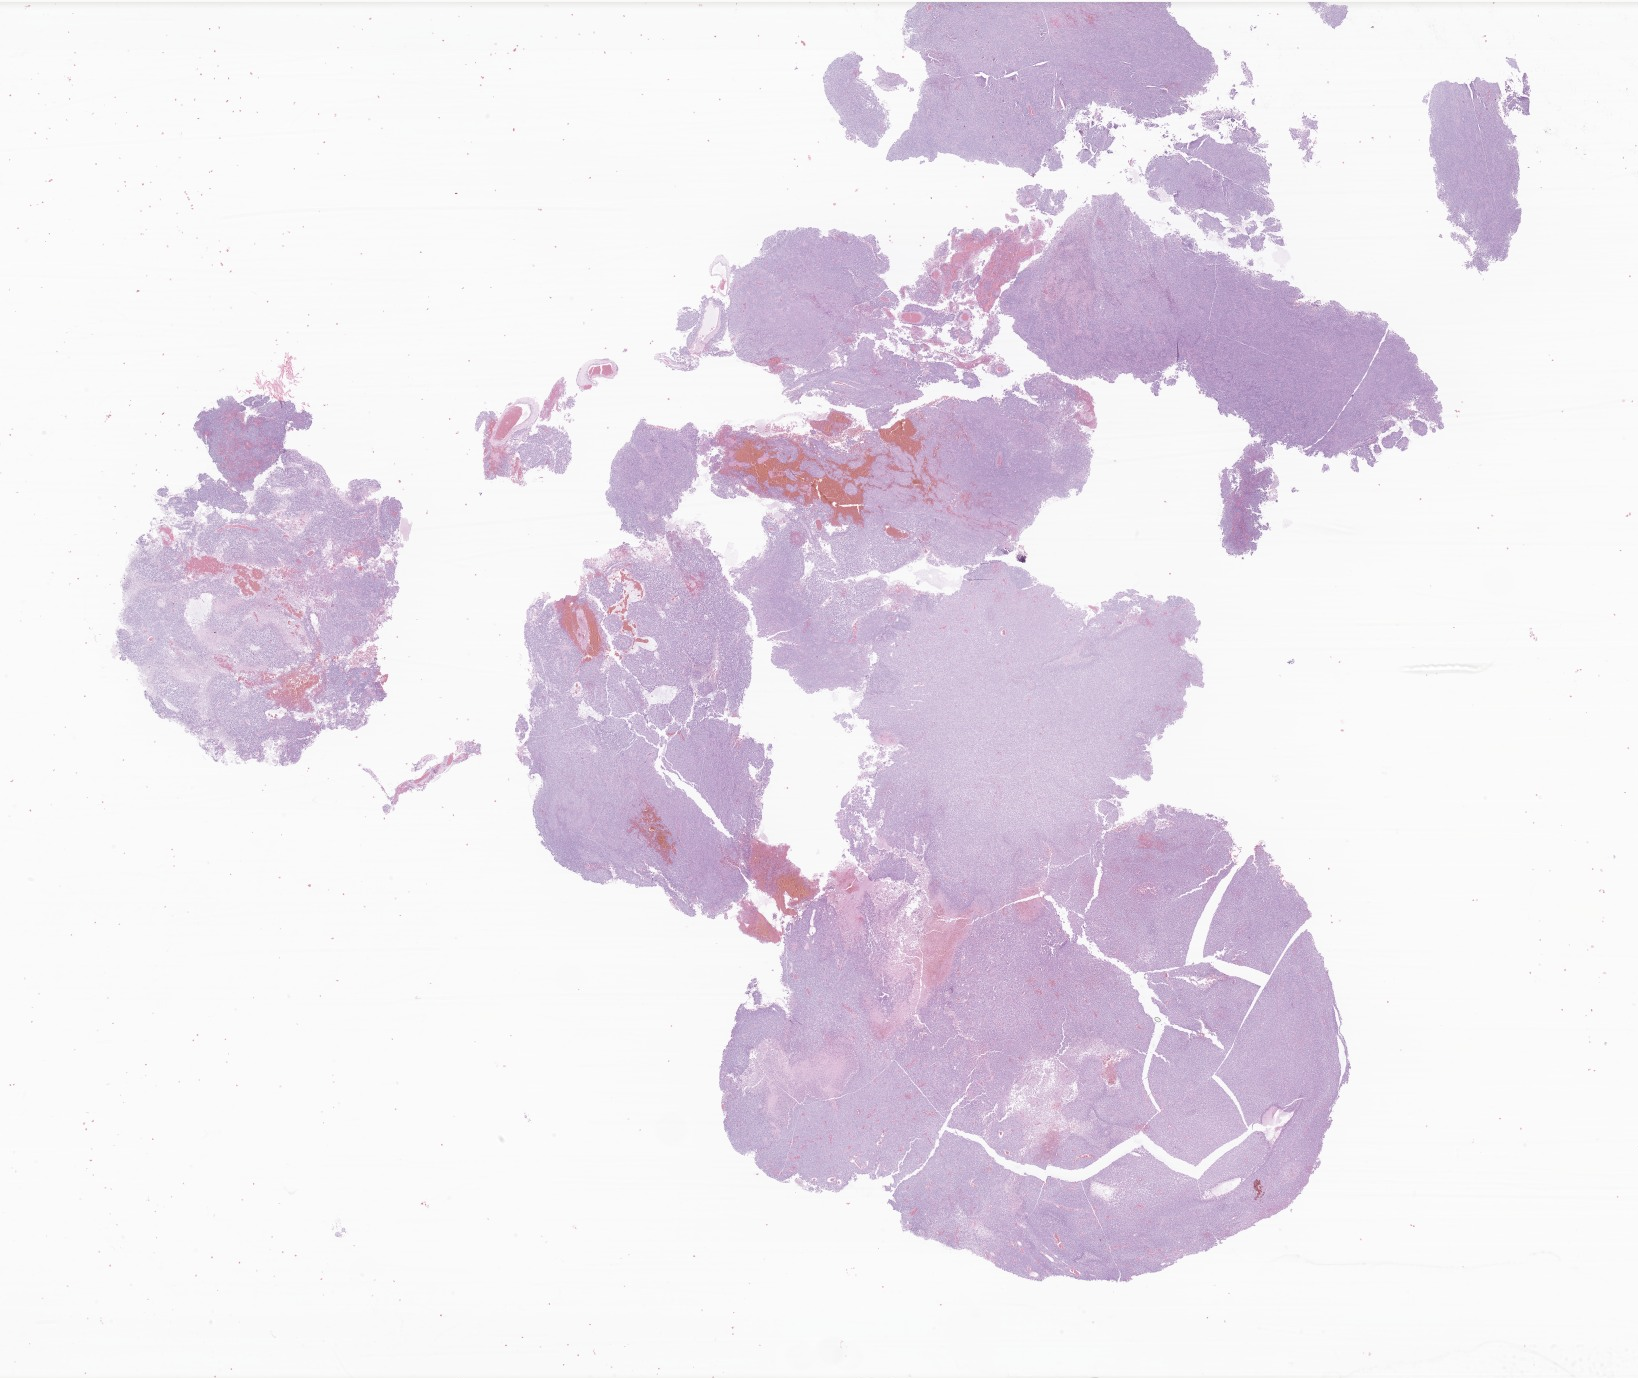
Digitized haematoxylin and eosin-stained section of tumor tissue from the frontal lobe — whole scanned area (about 27.6 x 23.2 mm) shown as a low-resolution overview, formalin-fixed paraffin-embedded section. Patient female; age 780 days (about 2.1 years).
Diagnosis (ICD-O-3 morphology term): Glioma, malignant.